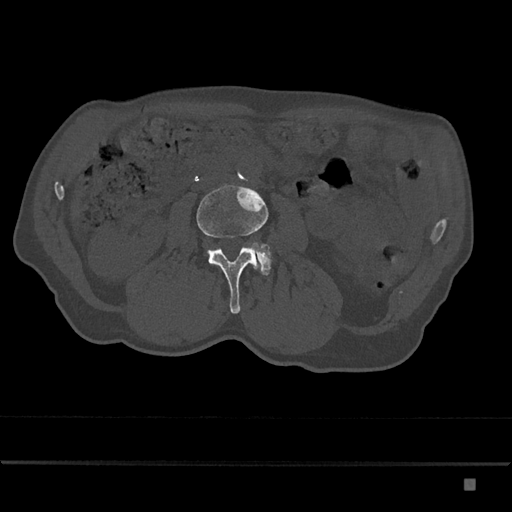
CT including the spine, one axial slice. Position 396 of 797 along the scan axis. Reconstruction kernel Br40s/3. 120 kVp. Bone window (W 1800 / L 400 HU). 512 × 512 image matrix. Male patient, age 72 years. Case-level facts recorded for this patient, not image findings: primary cancer: prostate.
Outlined on this slice (semi-automatically segmented with operator editing):
- L3 vertebra: bounding box (x1, y1, x2, y2) in pixels: (197, 185, 269, 314)
- L4 vertebra: (242, 244, 272, 275)